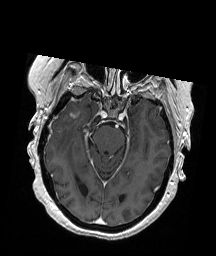
Brain MRI from a brain-tumour surgery series, one axial slice. T1-weighted post-contrast. 1 mm slice thickness. 216 × 256 image matrix, field of view 211 × 250 mm. From the clinical record (not read from this slice): histopathology: Glioblastoma; WHO grade: 4; IDH mutation: no; tumour location: Right Temporal.
Annotated regions visible in this slice (manually delineated by an expert):
- tumour: bounding box [x1, y1, x2, y2] px = [55, 112, 79, 139]